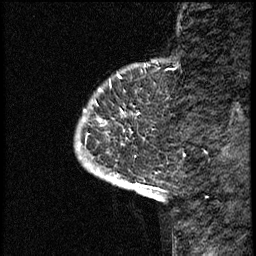
Breast MRI (dynamic contrast-enhanced), one sagittal slice. Position 6 of 68 along the scan axis. Dynamic contrast-enhanced study with each time point stored as its own series, time point 2 of 3 at this slice position (early post-contrast, ordered by acquisition time). 1.5 T. TE 4.2 ms, TR 17.6 ms. 2 mm slice thickness. 256 × 256 image matrix, field of view 200 × 200 mm. Female patient, age 52 years. From the clinical record (not read from this slice): setting: breast cancer imaged before/during neoadjuvant chemotherapy; receptor status: HER2-positive.
Annotated regions visible in this slice (semi-automatically segmented with operator editing):
- analysis volume of interest (the breast-tissue region the enhancement analysis was run in; not a lesion): box from (x=75, y=61) to (x=176, y=184) px
- tumour enhancement mask (voxels above the 100 % enhancement threshold inside the analysis volume of interest): (x=113, y=176)–(x=127, y=184)